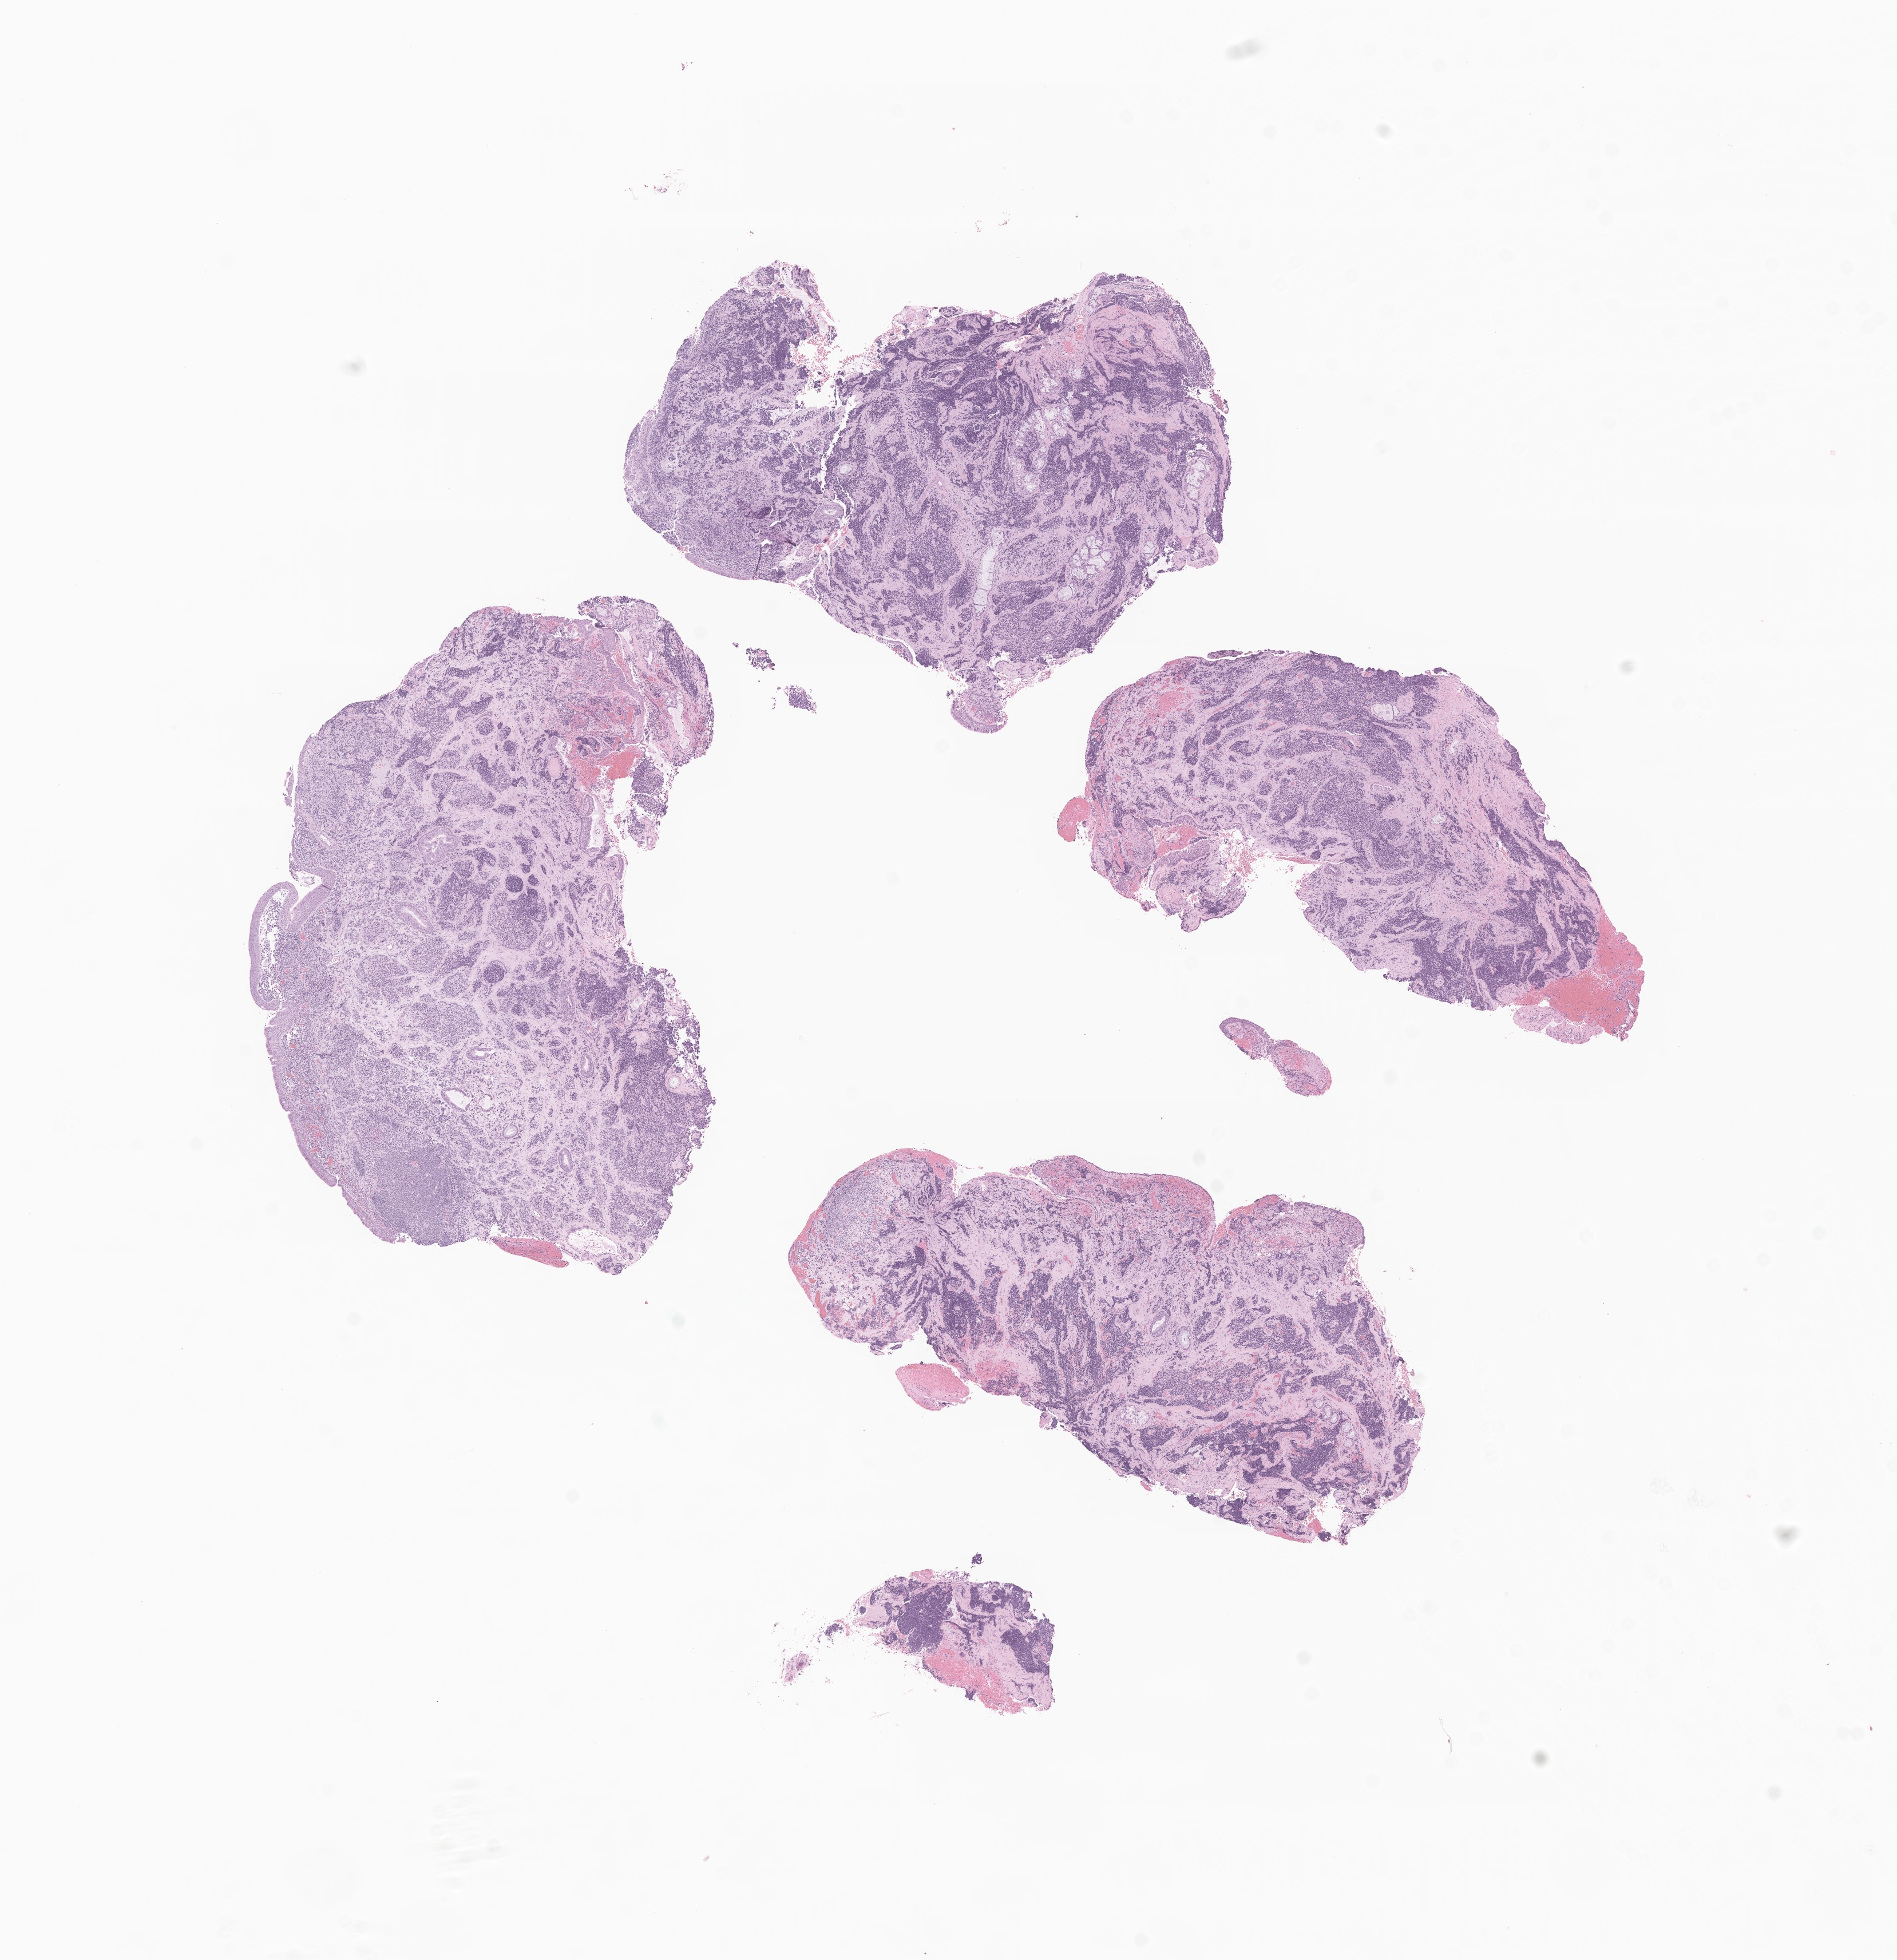
H&E whole-slide image of tumor tissue from the nasopharynx — whole scanned area (about 14.0 x 14.4 mm) shown as a low-resolution overview. Formalin-fixed paraffin-embedded section. Patient male; age 35 months.
• diagnosis (ICD-O-3 morphology term): Rhabdomyosarcoma, NOS